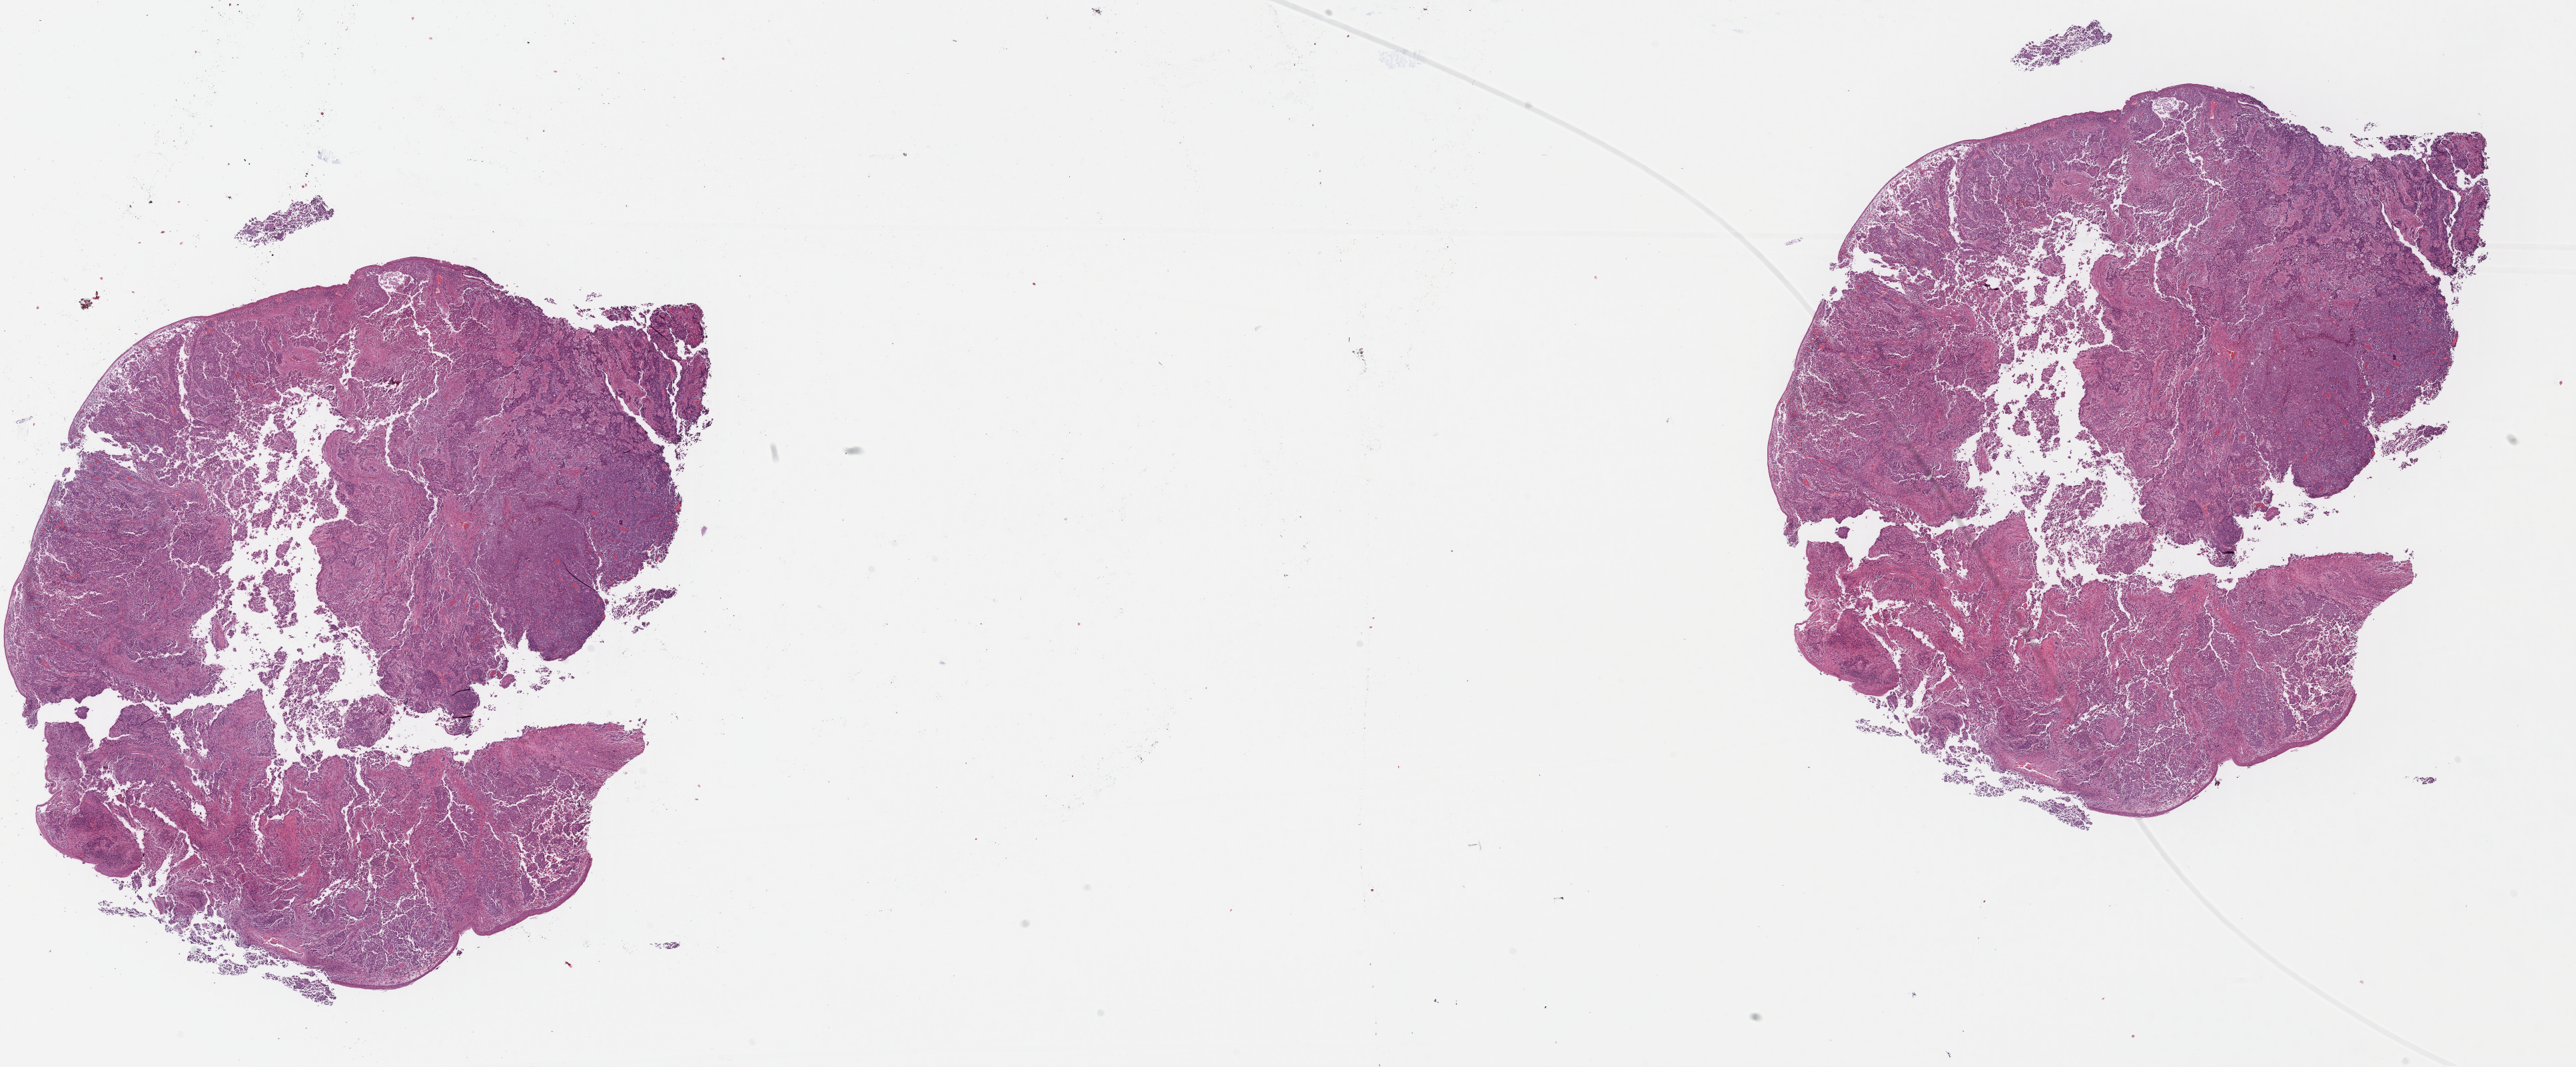
Digitized H&E-stained tissue section (whole slide), shown as a low-resolution overview of the whole scanned area (about 30.4 x 12.6 mm, slide scanned at 40x); formalin-fixed paraffin-embedded (FFPE) diagnostic section; primary tumour sample from the cervix. Female patient; age at initial diagnosis 34 years. Histologic grade: G3 (poorly differentiated).
Histologic diagnosis: Squamous cell carcinoma, NOS (ovary). FIGO stage: IVB.